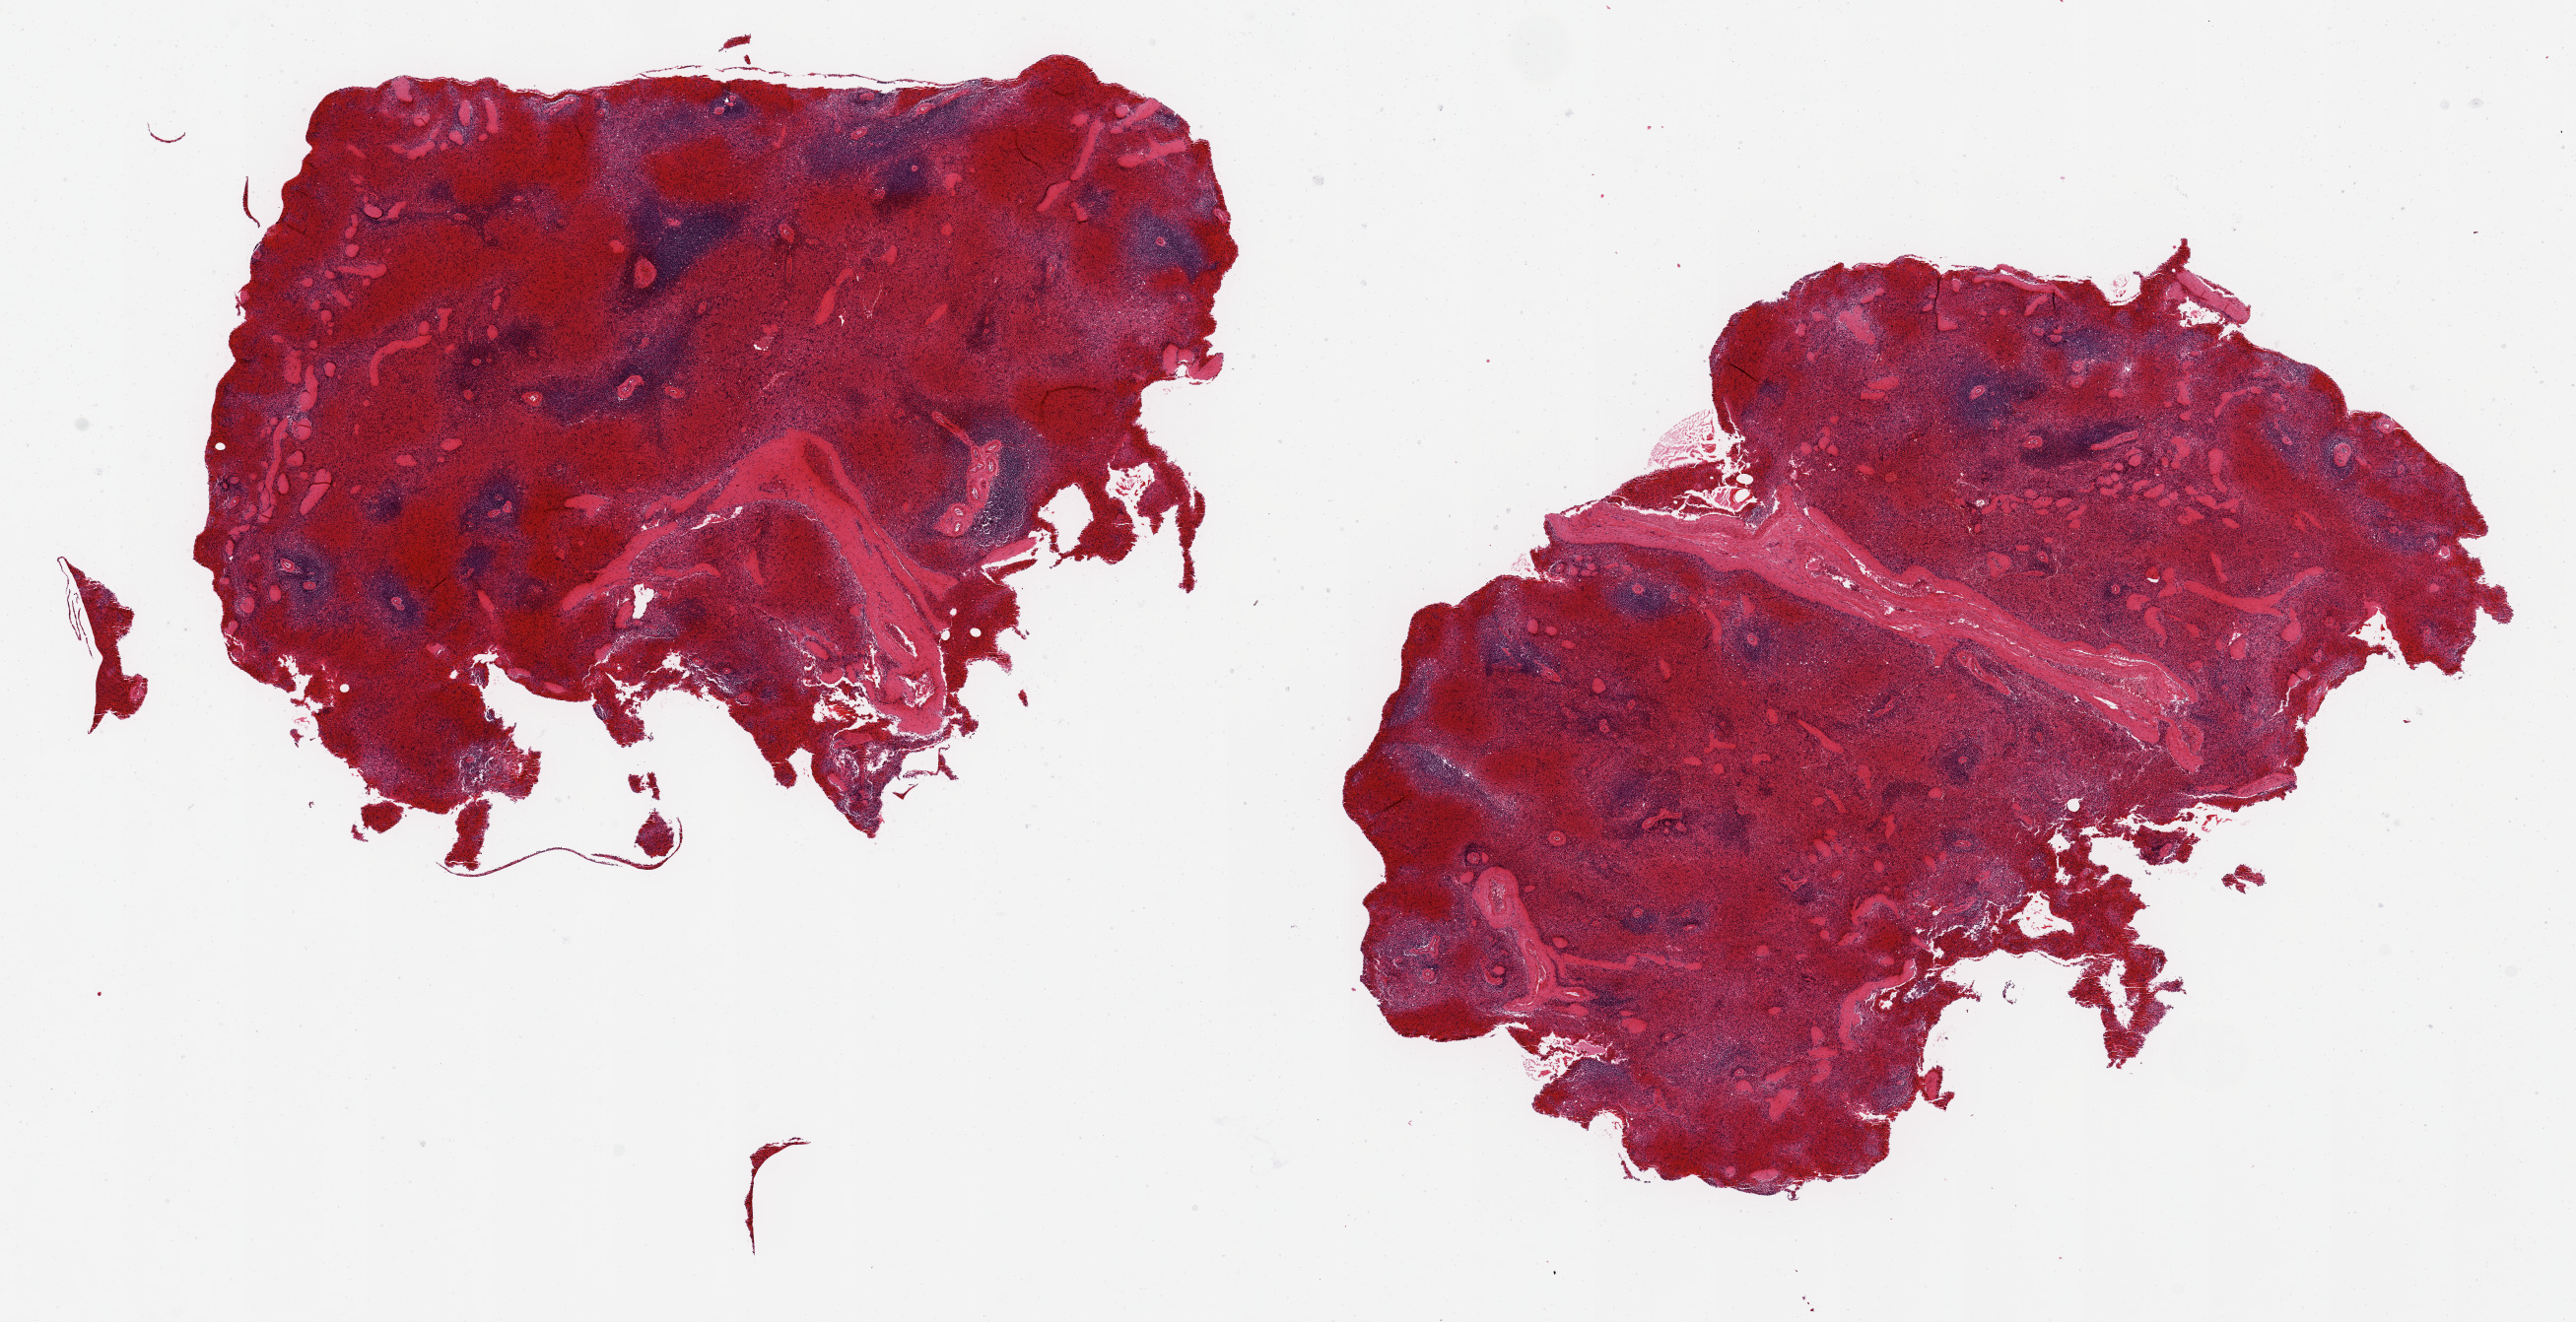
Whole-slide image, H&E stain, brightfield — whole scanned area (about 20.7 x 10.6 mm) shown as a low-resolution overview; PAXgene-fixed paraffin-embedded (PFPE) section; section of spleen (target tissue); donor tissue sample. Donor sex: male.
Pathologist's review note for this sample: 2 ~7x6.5mm aliquots.